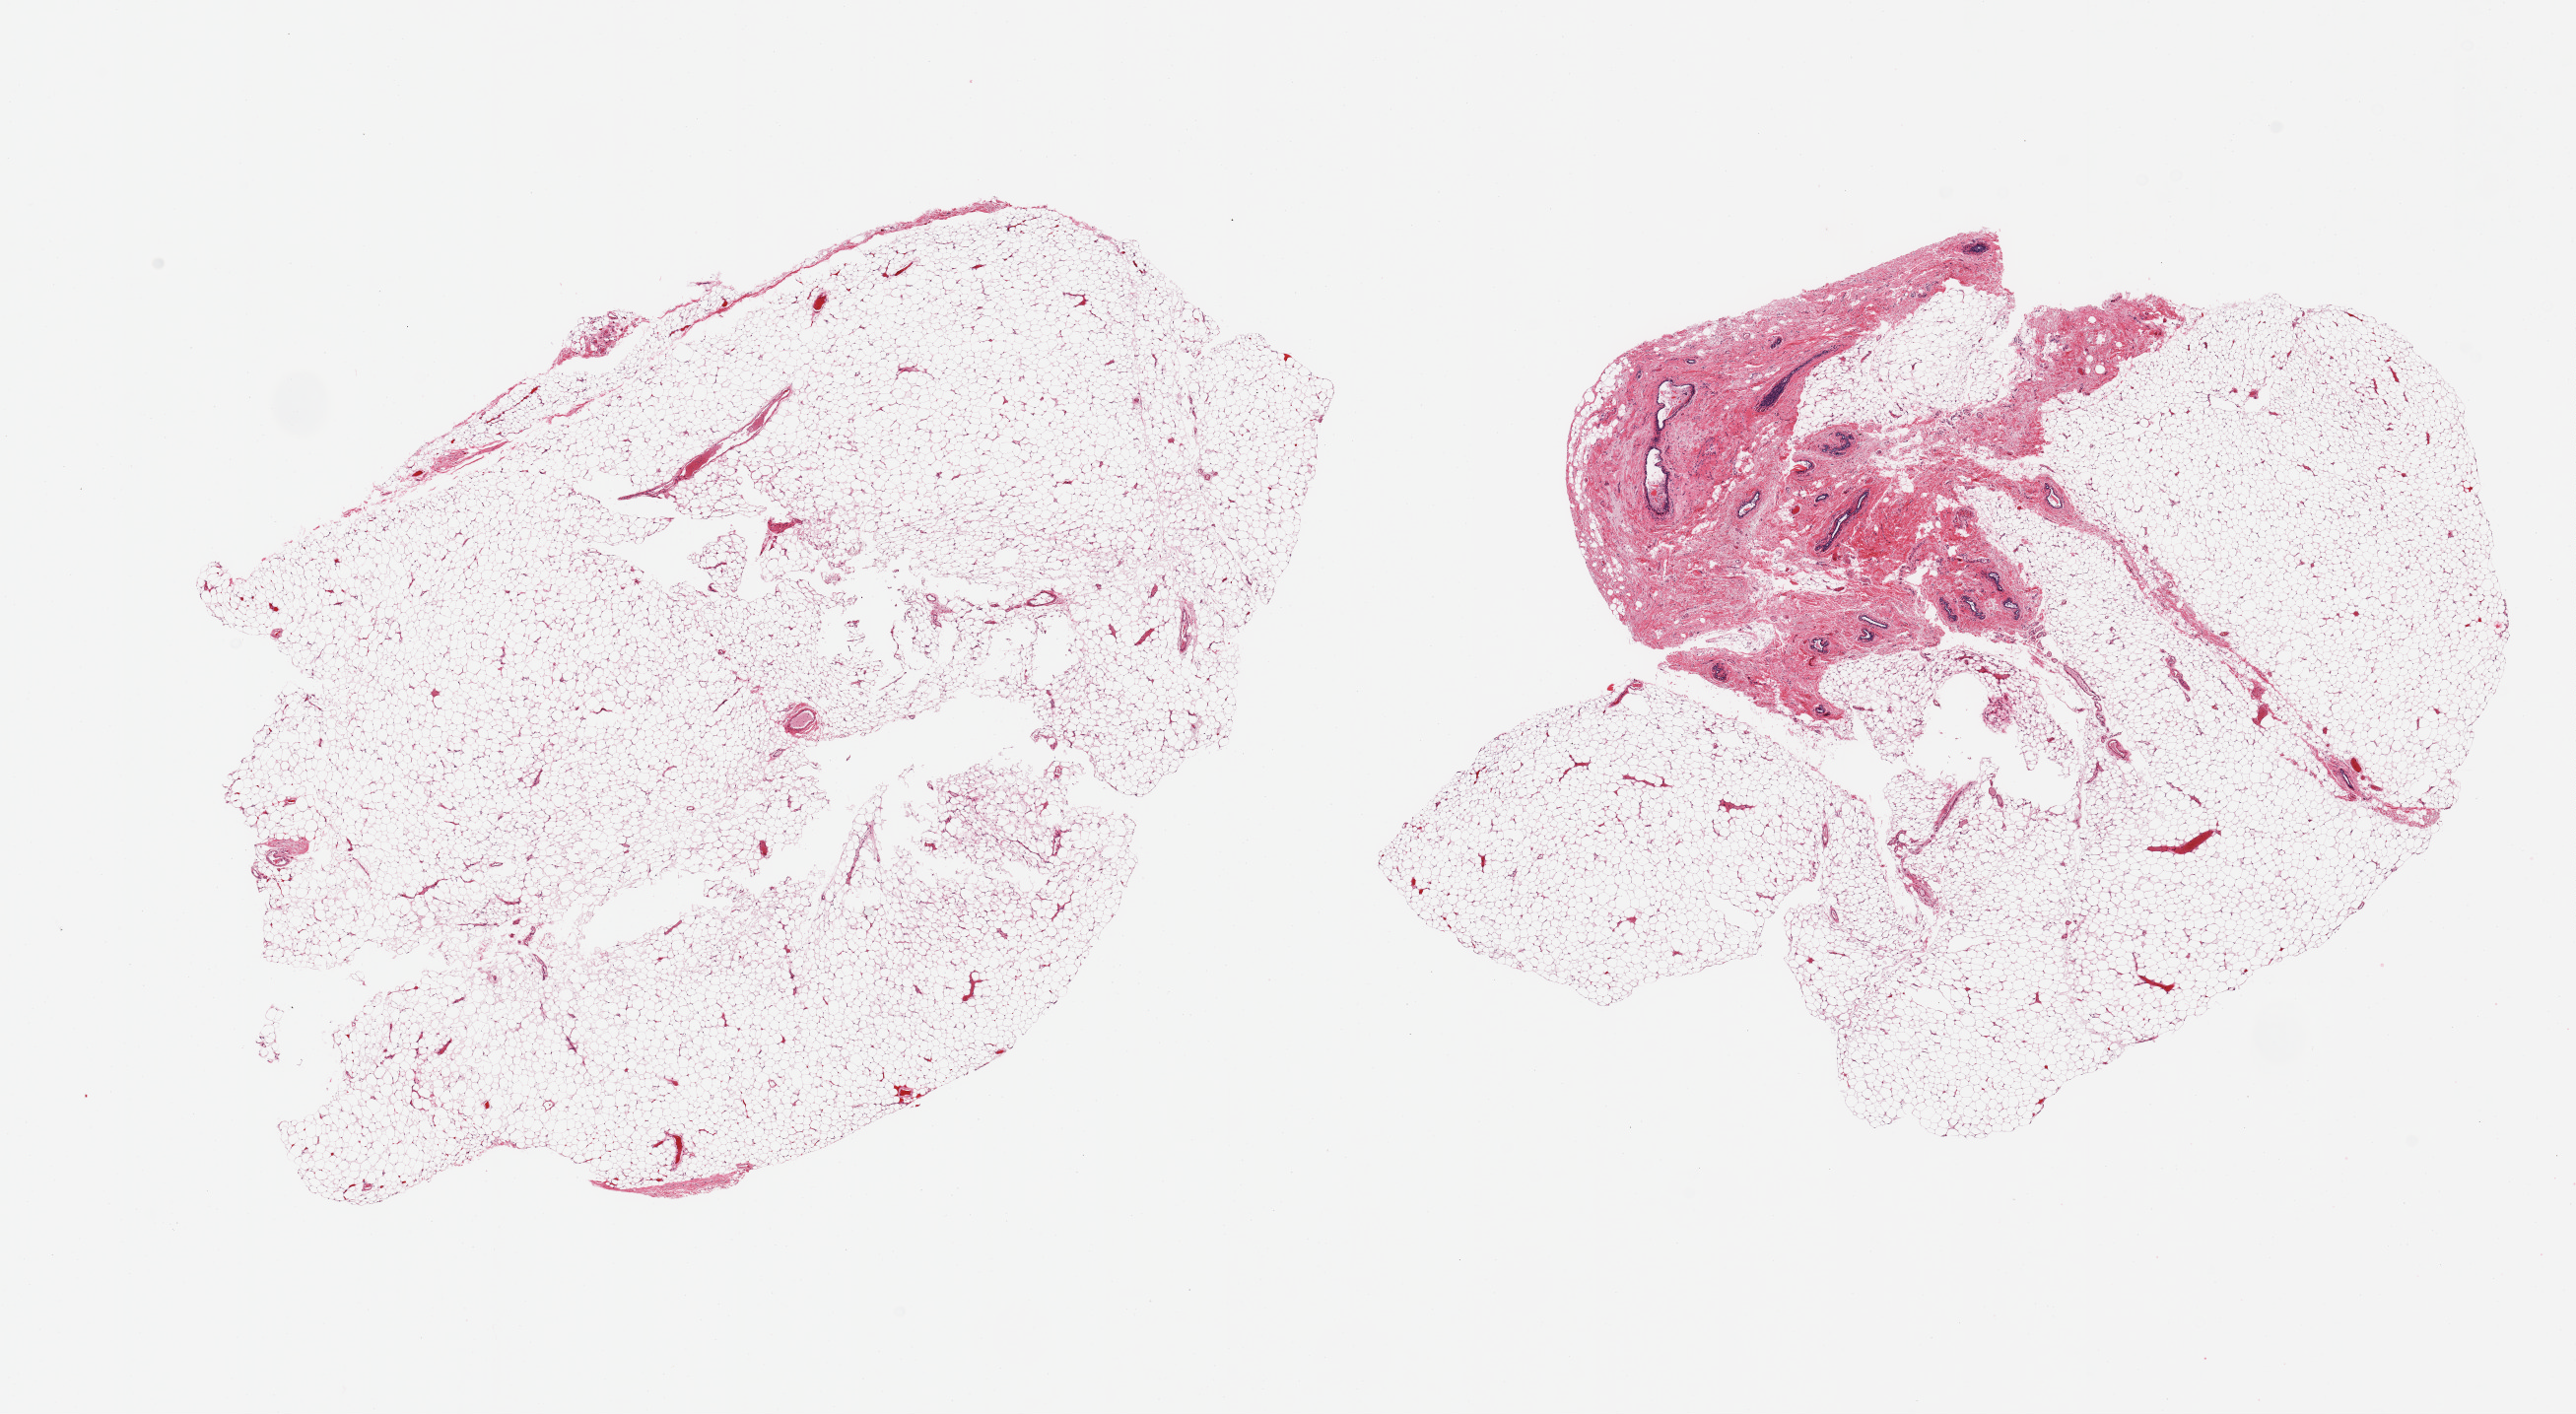
Hematoxylin and eosin (H&E) whole-slide image — a low-resolution overview of the entire scanned area, about 20.7 x 11.3 mm. PAXgene-fixed paraffin-embedded (PFPE) section. Section of breast (target tissue). Donor tissue sample. Female donor.
Reviewer comment on this tissue sample: 2 pieces; atrophic ducts and lobules in 1, all adipose in other.